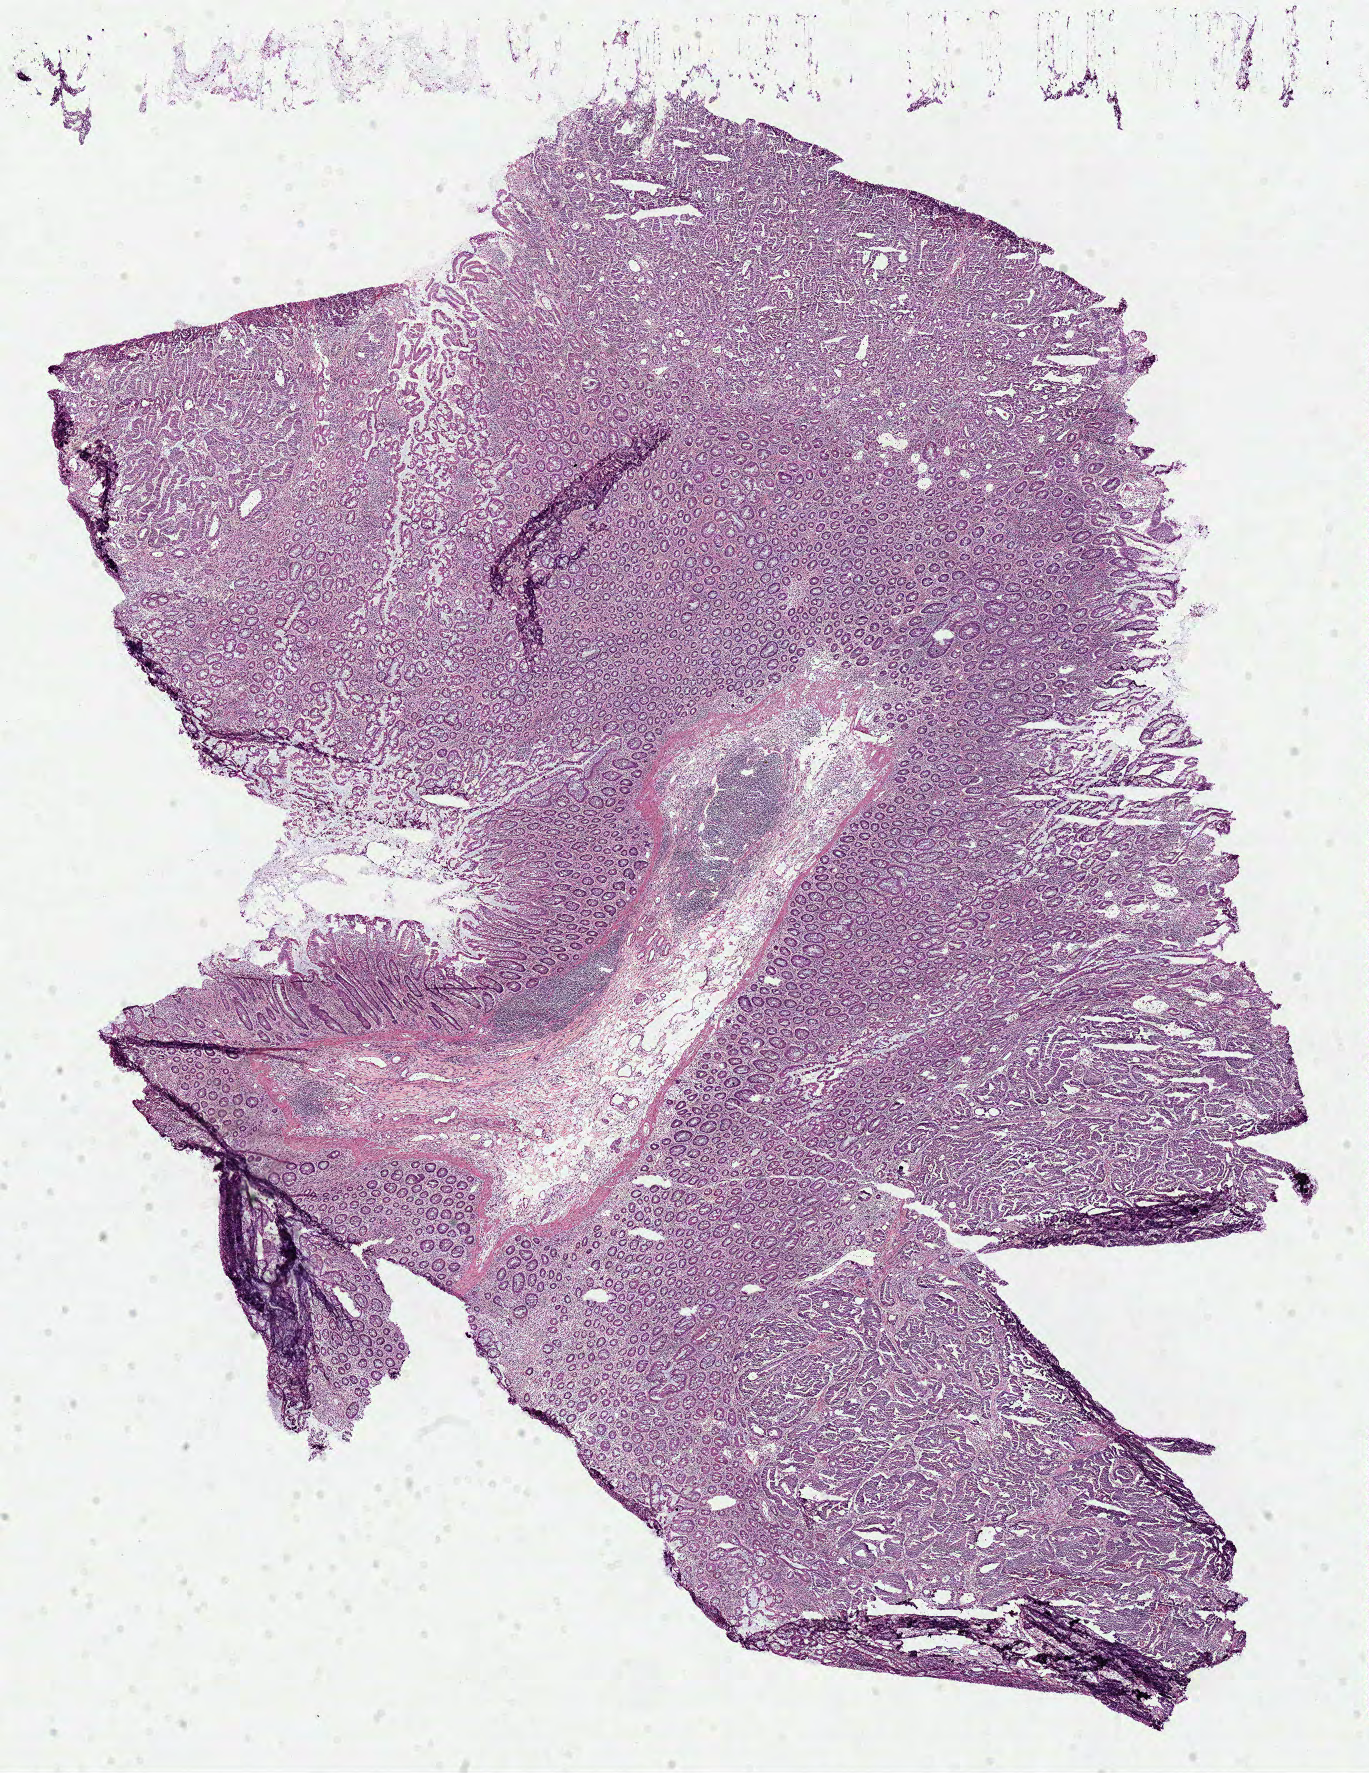
Digitized H&E-stained tissue section (whole slide) — whole scanned area (about 10.8 x 13.9 mm) shown as a low-resolution overview; frozen section from the top of the tissue portion; primary tumour sample from the colon. Patient sex: male. Composition of this section per pathologist review: tumour cells 54%, tumour nuclei 60%, normal cells 35%, stromal cells 10%, necrosis 1%.
Histologic diagnosis: Adenocarcinoma, NOS. AJCC pathologic stage: IIIB. TNM: T4a N1 MX.